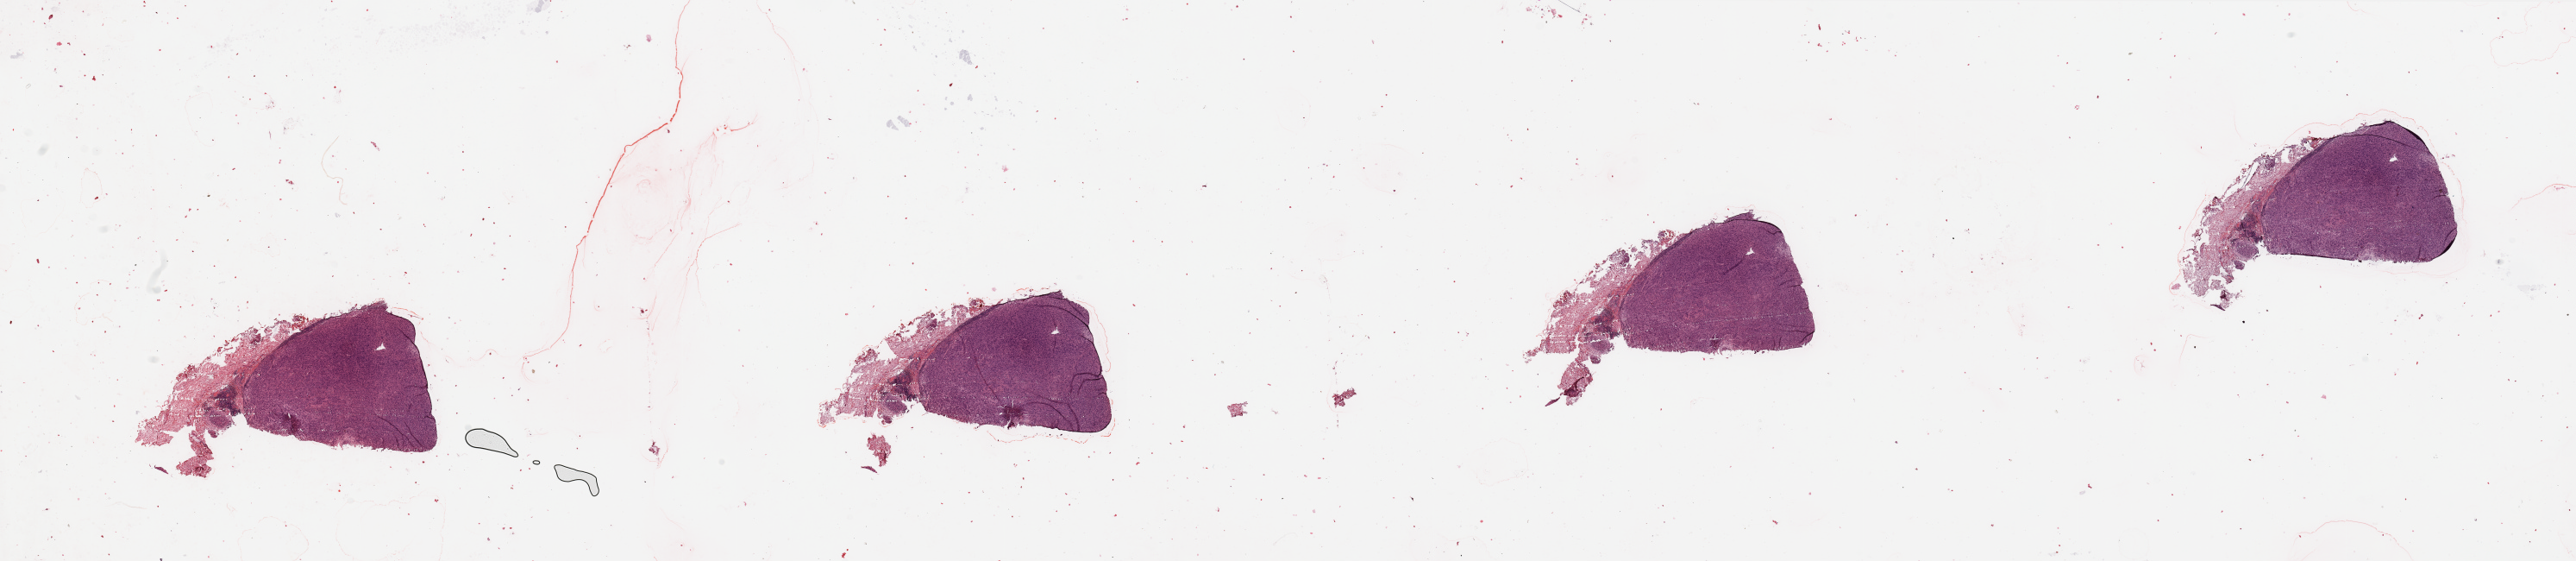
Digitized H&E-stained tissue section (whole slide), whole scanned area (about 47.3 x 10.3 mm) shown as a low-resolution overview; tumour tissue sample, sampled site: lymph node. Patient: male, age 84 years. Slide review estimates, as recorded: tumour nuclei 95%, necrosis 0%.
This section: metastatic tumour tissue. Patient diagnosis: Malignant melanoma, NOS.